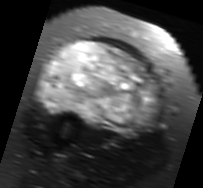
MRI of an extremity soft-tissue mass, one axial slice. Slice 38 of 91 in the series (ordered by position). T2-weighted fat-saturated. MR volume resampled by the dataset authors to the PET/CT grid (not the native acquisition matrix). 3.27 mm slice thickness. 203 × 188 image matrix, field of view 198 × 184 mm. Female patient. Case-level facts recorded for this patient, not image findings: histological type: malignant solitary fibrous tumor; grade: intermediate; site of the primary tumour: right thigh.
Outlined on this slice (expert contour drawn on MRI and transferred to this co-registered scan by the dataset authors):
- gross tumour volume including surrounding oedema: bounding box (x1, y1, x2, y2) in pixels: (35, 40, 162, 136)
- gross tumour volume (mass): (42, 40, 157, 132)